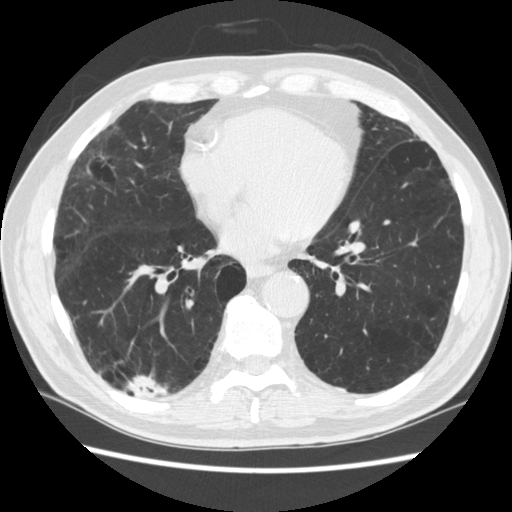
Low-dose screening chest CT, one axial slice; slice 112 of 266 in the series (ordered by position); reconstruction kernel STANDARD; lung window (W 1500 / L -600 HU); 512 × 512 image matrix, field of view 360 × 360 mm.
Annotated regions visible in this slice (manually delineated by an expert):
- lesion 1 (tumor, upper lobe of right lung): box from (x=128, y=376) to (x=166, y=397) px